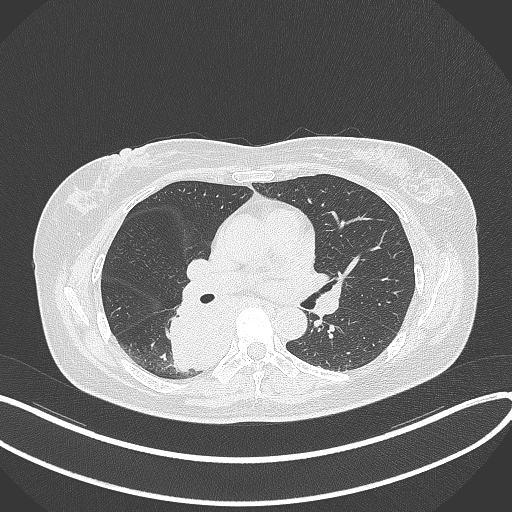
Chest CT, one axial slice; 120 kVp; lung window (W 1500 / L -600 HU); 1 mm slice thickness; 512 × 512 image matrix. Patient: female, 54 years. From the clinical record (not read from this slice): clinical TNM (as recorded): T4 N0 M0.
Structures marked on this image (rectangle marked by the reading radiologist):
- lung tumour (recorded histology: adenocarcinoma): box from (x=161, y=297) to (x=237, y=373) px